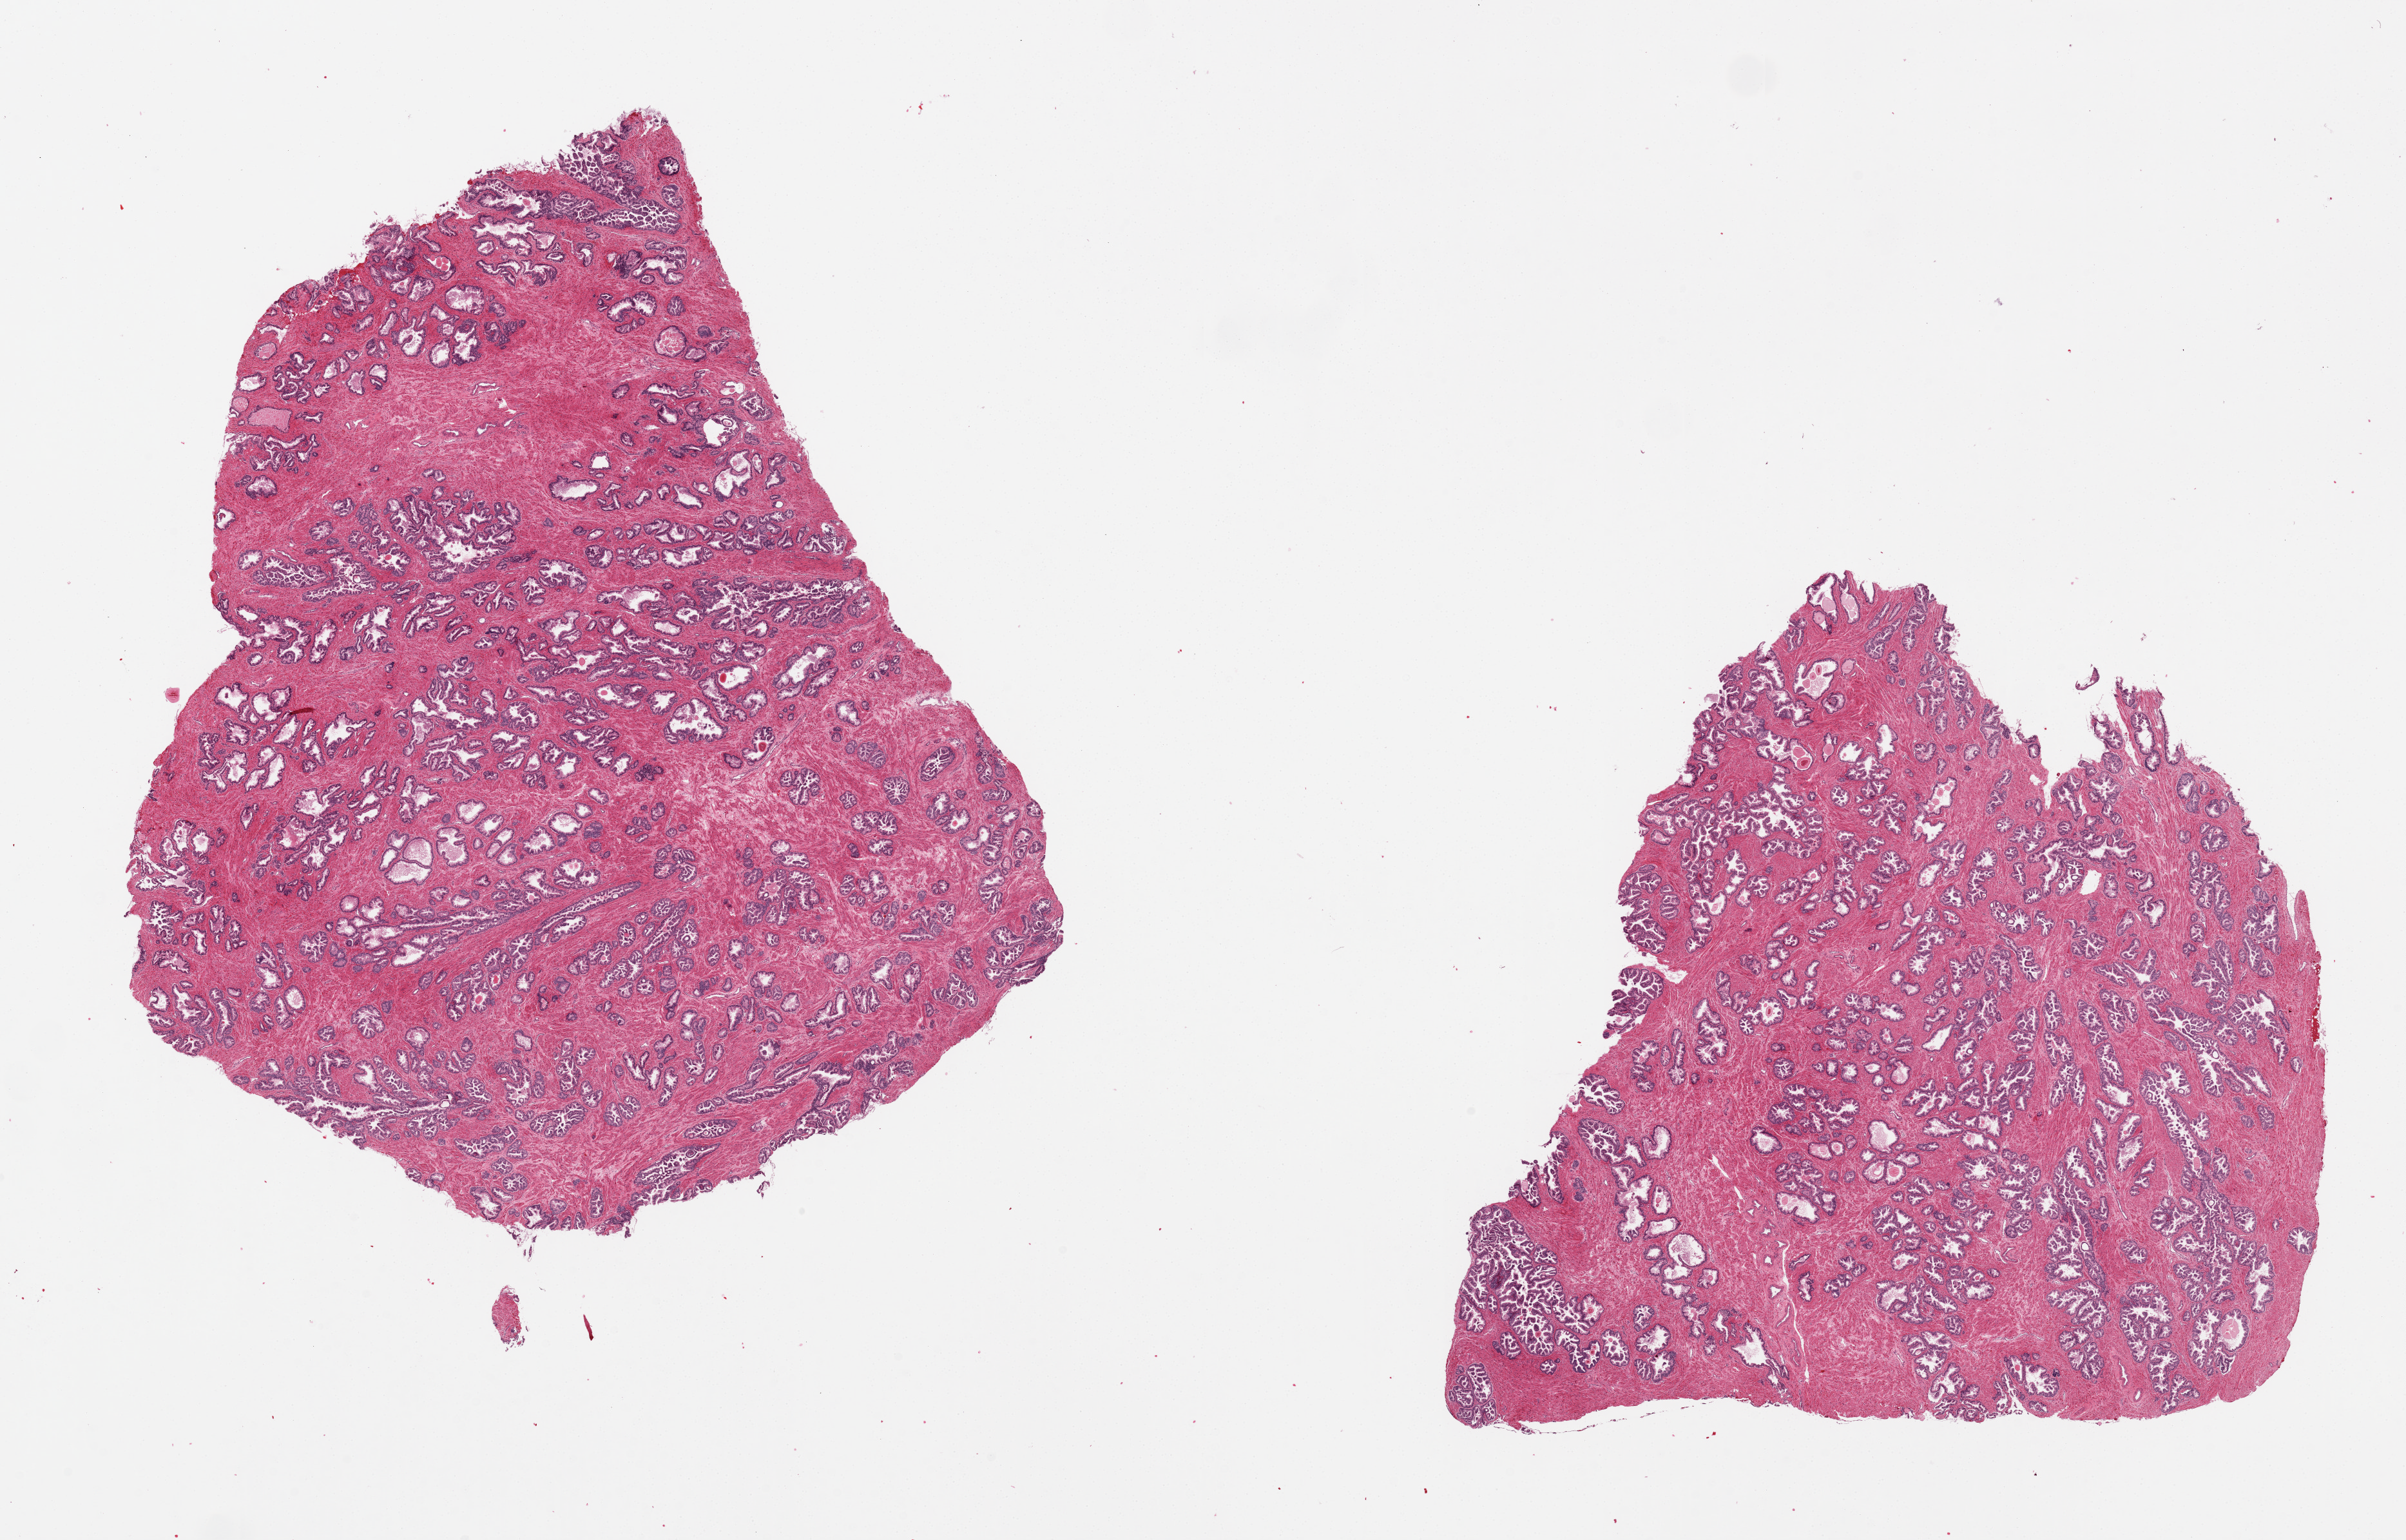
Hematoxylin and eosin (H&E) whole-slide image, brightfield — whole scanned area (about 29.5 x 18.9 mm, slide scanned at 20x) shown as a low-resolution overview, PAXgene-fixed paraffin-embedded (PFPE) section, section of prostate (target tissue), tissue donor sample. Male donor.
Review note (as recorded): 2 pieces, well preserved; diffuse glandular hyperplasia.